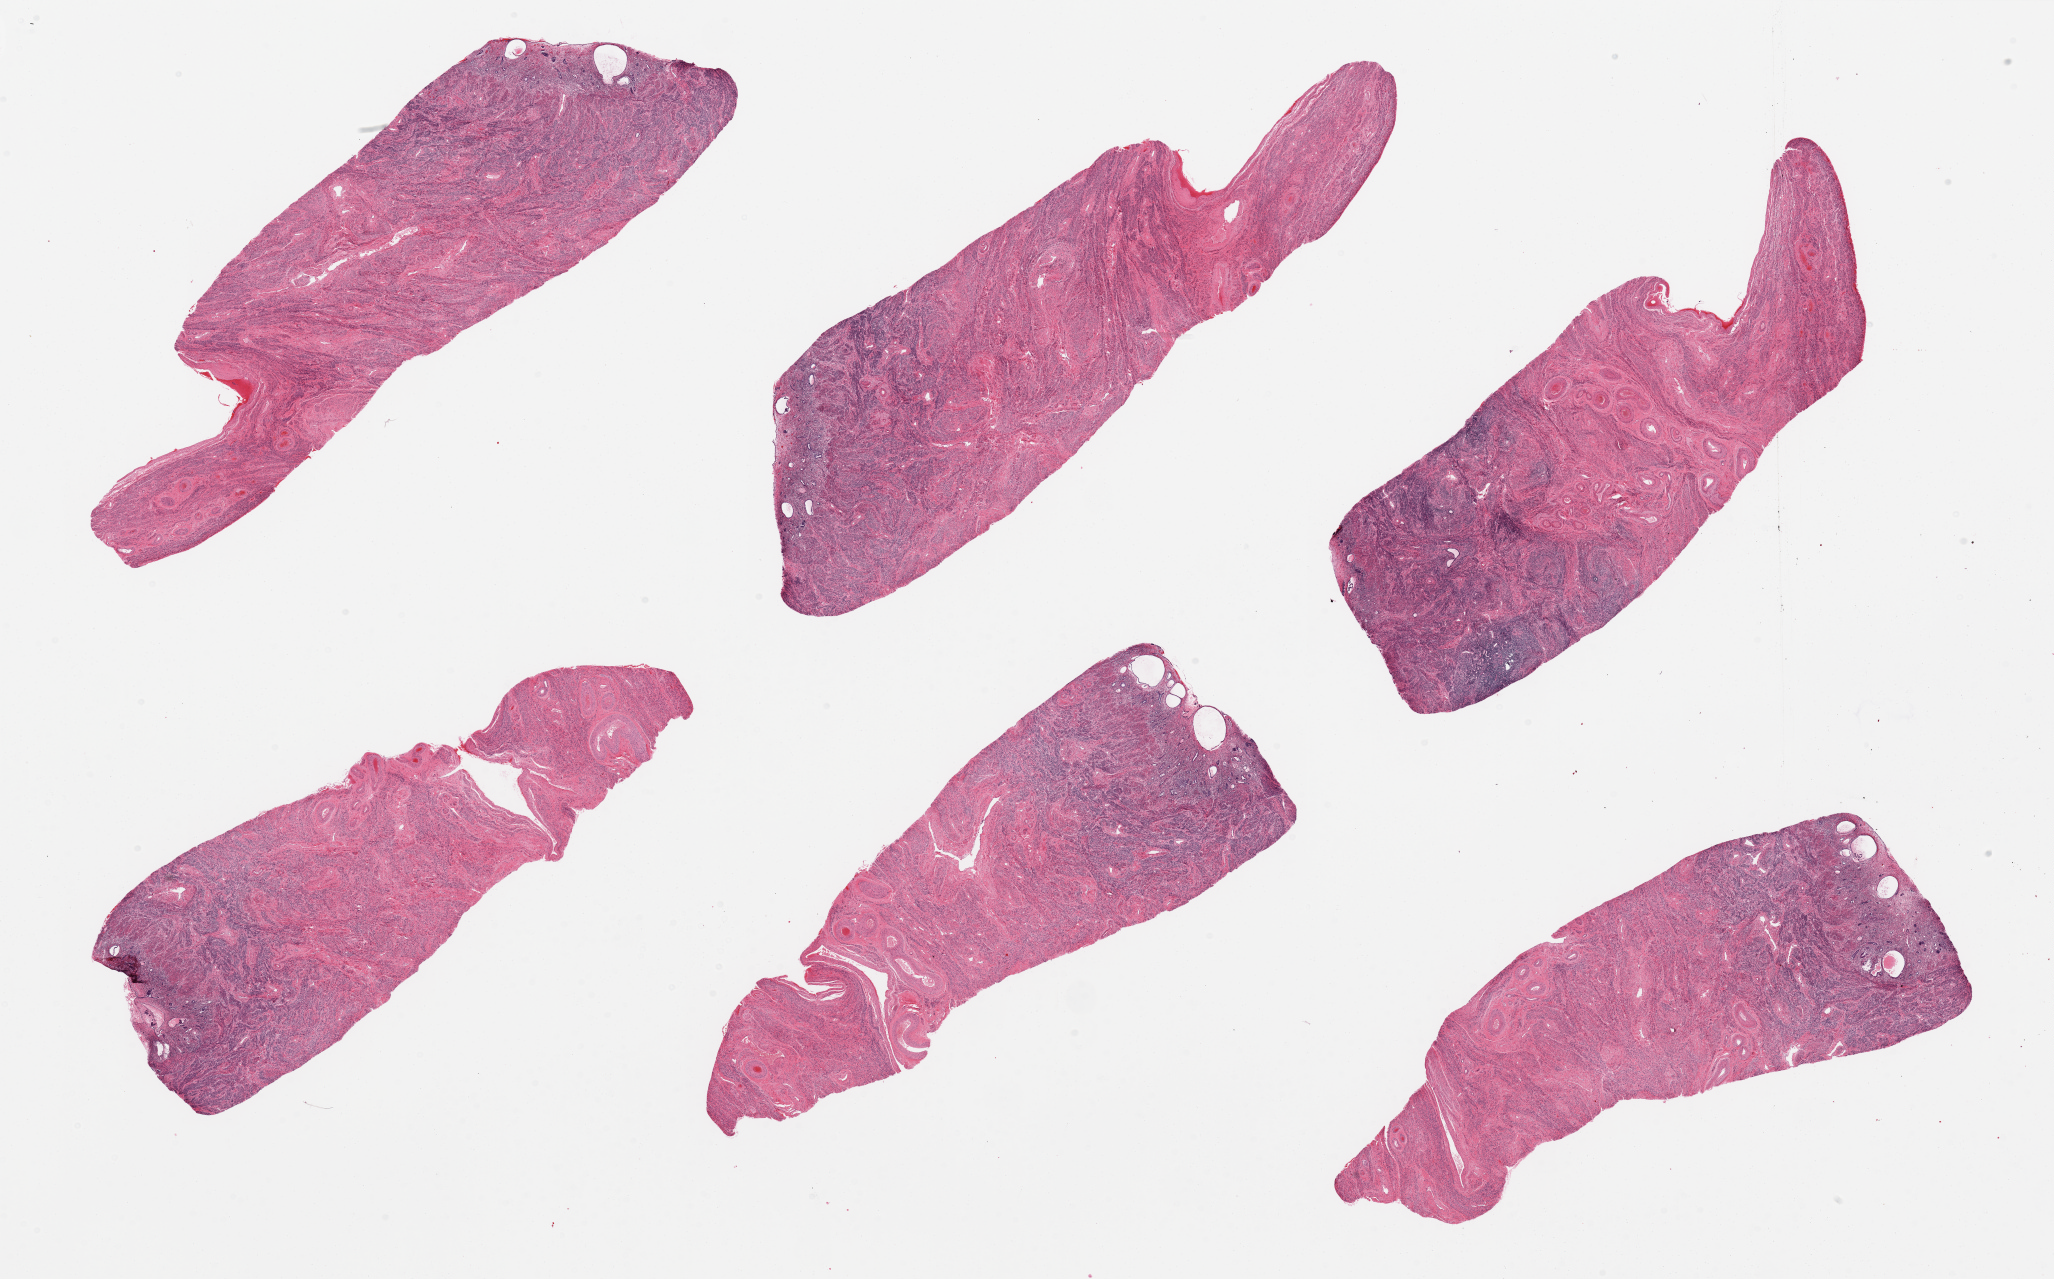
Whole-slide image, haematoxylin and eosin stain — shown as a low-resolution overview of the whole scanned area (about 32.5 x 20.2 mm, from a 20x scan). PAXgene-fixed paraffin-embedded (PFPE) section. Sampled site (target tissue): uterus. Donor tissue sample. Donor sex: female.
* pathologist's review note for this sample: 6 pieces, mainly myometrium, atophic endometrium with cystic change present, ~1mm thick